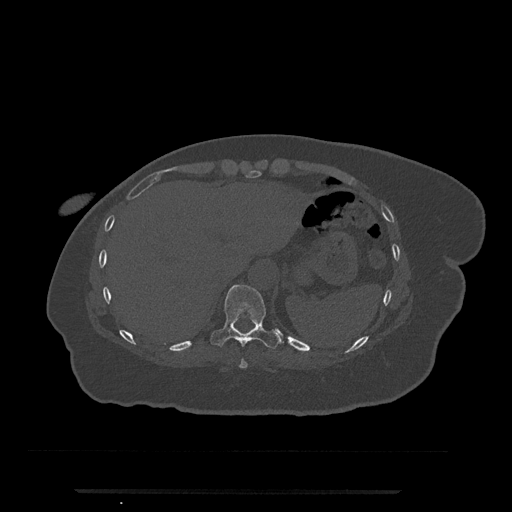
CT including the spine, one axial slice; slice 291 of 797 in the series (ordered by position); 120 kVp; bone window (W 1800 / L 400 HU); 512 × 512 image matrix, field of view 440 × 440 mm. Female patient, age 51 years. Case-level facts recorded for this patient, not image findings: primary cancer: neuro; vertebrae with lytic lesions (as recorded): T8.
Outlined on this slice (semi-automatic segmentation, software-assisted and operator-edited):
- T10 vertebra: bounding box (x1, y1, x2, y2) in pixels: (210, 285, 280, 349)
- T9 vertebra: (239, 359, 248, 369)